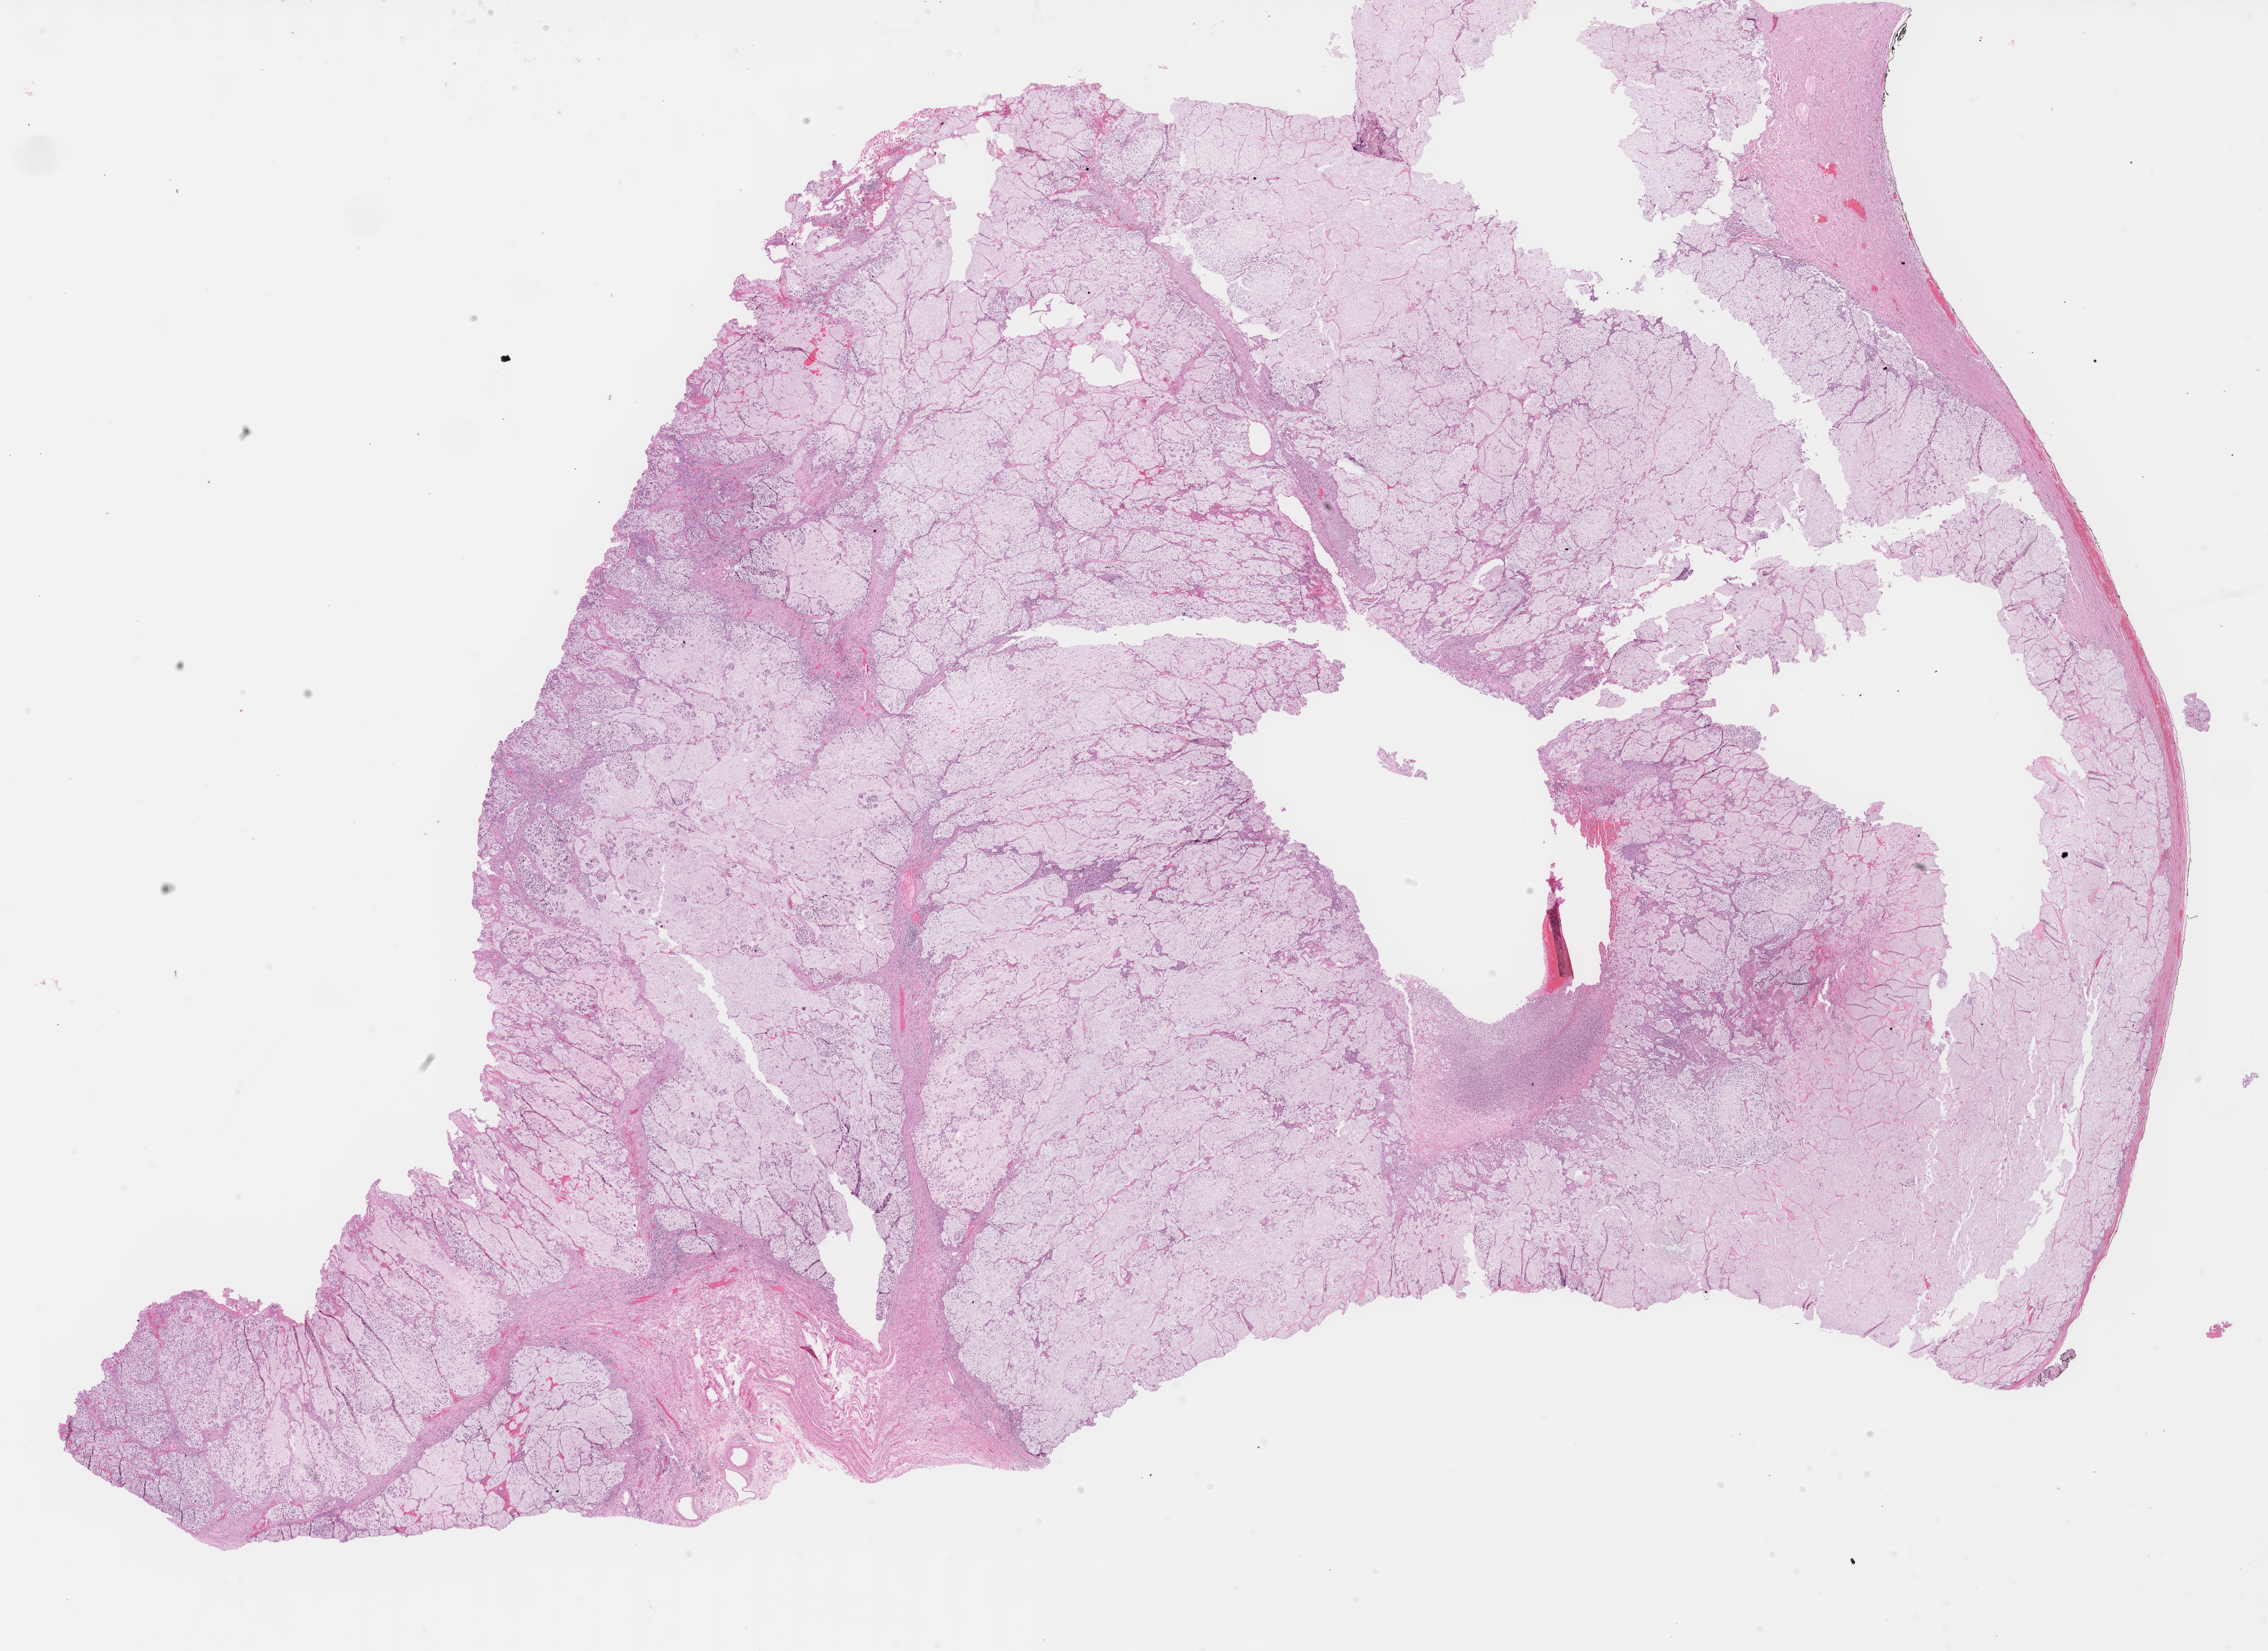
Whole-slide histology image, Hematoxylin and eosin (H&E) stained — whole scanned area (about 28.7 x 20.9 mm, acquisition: 40x scan) shown as a low-resolution overview, formalin-fixed paraffin-embedded (FFPE) diagnostic section, primary tumour sample from the colon. Patient: female, age at initial diagnosis 52 years.
Diagnosis: Mucinous adenocarcinoma (cecum).